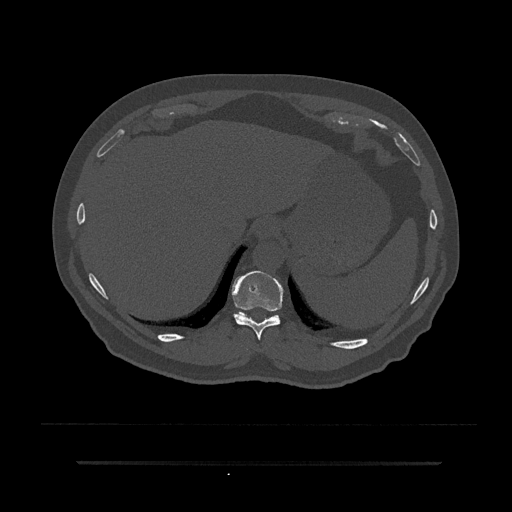
CT including the spine, one axial slice. Position 316 of 797 along the scan axis. Reconstruction kernel Br40s/3. Bone window (W 1800 / L 400 HU). 512 × 512 image matrix. Male patient, age 59 years. Case-level facts recorded for this patient, not image findings: primary cancer: bile ducts.
Structures marked on this image (semi-automatically segmented with operator editing):
- T10 vertebra: bounding box [x1, y1, x2, y2] px = [232, 271, 283, 340]
- T11 vertebra: [236, 312, 279, 319]